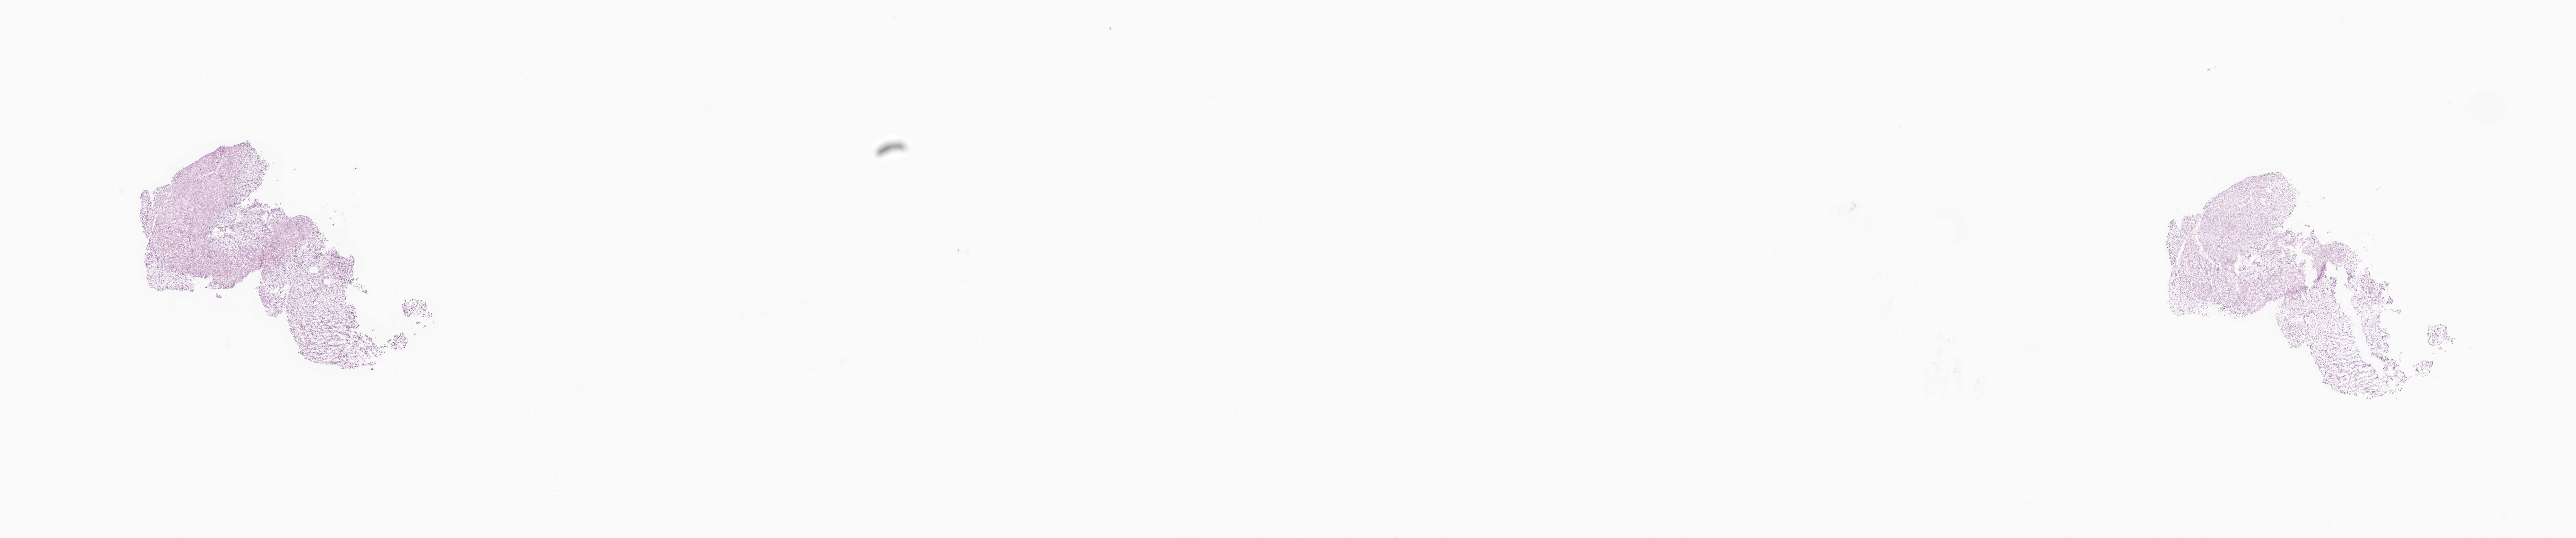
Digitized H&E-stained section of tumor tissue from the cerebellum, shown as a low-resolution overview of the whole scanned area (about 33.8 x 7.1 mm). Cryosection (OCT / tissue freezing medium). Patient male; age 152 months (12 years 8 months).
- diagnosis: Pilocytic astrocytoma